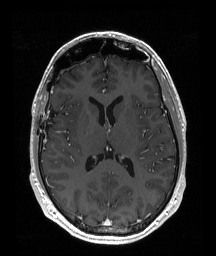
Brain MRI from a brain-tumour surgery series, one axial slice. Slice 95 of 192 in the series (ordered by position). T1-weighted post-contrast. 1 mm slice thickness. 216 × 256 image matrix, field of view 219 × 260 mm. From the clinical record (not read from this slice): histopathology: Astrocytoma; WHO grade: 2; IDH mutation: yes.
Structures marked on this image (manually delineated by an expert):
- tumour: bounding box <71,112,79,120> (left, top, right, bottom; pixels)